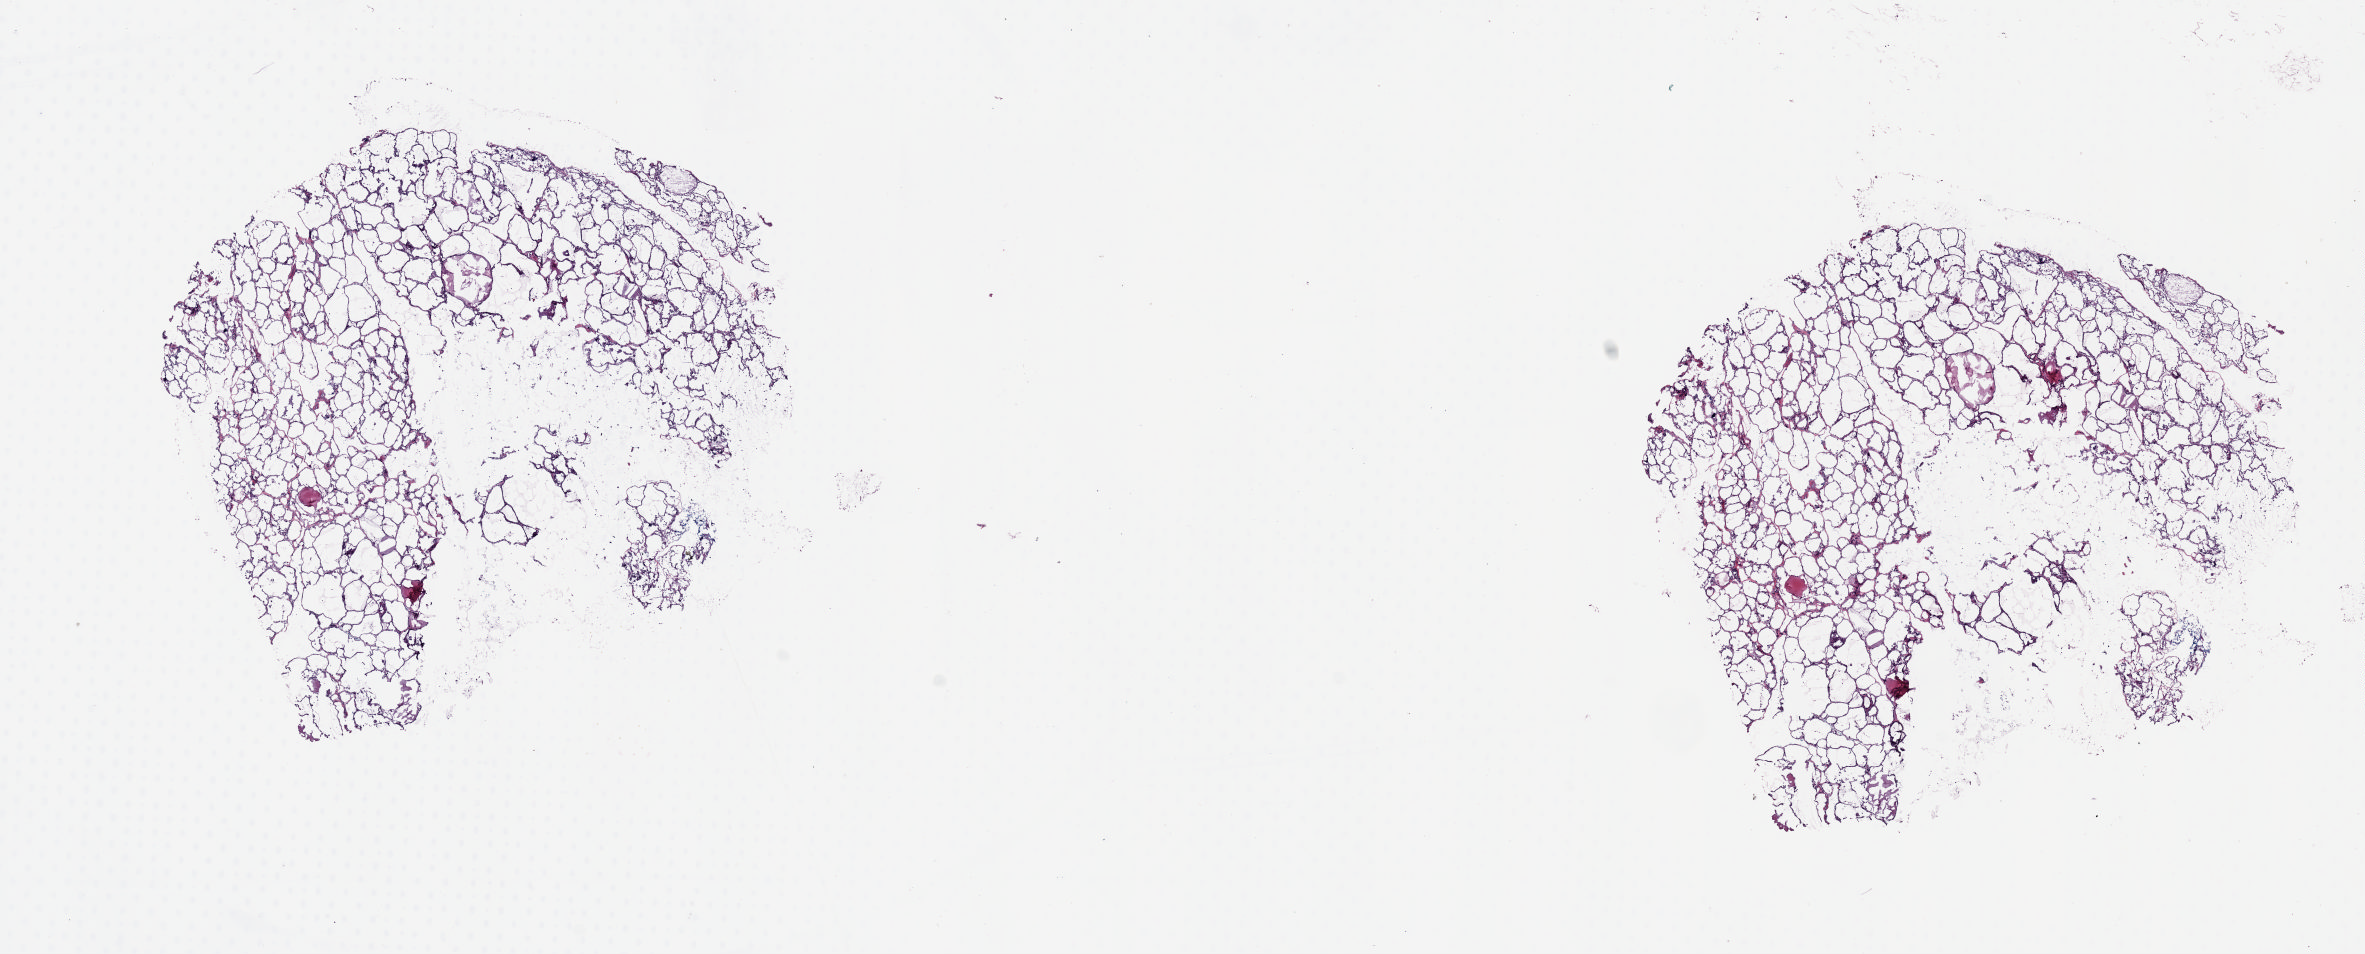
Hematoxylin and eosin (H&E) stained whole-slide image — shown as a low-resolution overview of the whole scanned area (about 18.6 x 7.5 mm), frozen section from the top of the tissue portion, solid tissue normal (non-tumour tissue) sample from the thyroid. Patient: female, age at initial diagnosis 61 years. Slide review estimates, as recorded: tumour cells 0%, tumour nuclei 0%, normal cells 100%, stromal cells 0%, necrosis 0%. Infiltration values recorded for this section: lymphocyte infiltration 2%, monocyte infiltration 5%, neutrophil infiltration 0%.
This section: solid tissue normal sample (biorepository sample class). Patient diagnosis: Papillary adenocarcinoma, NOS (thyroid gland).